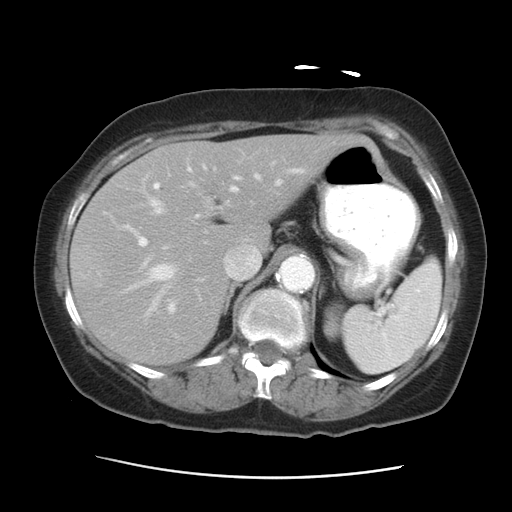
Contrast-enhanced abdominal CT, one axial slice; position 20 of 29 along the scan axis; reconstruction kernel STANDARD; intravenous contrast given; soft-tissue window (W 400 / L 40 HU); 7.5 mm slice thickness; 512 × 512 image matrix. Female patient, age 64 years. Case-level facts recorded for this patient, not image findings: diagnosis: colorectal cancer liver metastases, imaged before liver resection; multiple liver metastases: no; largest metastasis: 2.5 cm; chemotherapy before resection: no.
Annotated regions visible in this slice (manually delineated by an expert):
- hepatic veins: bounding box <125,161,305,315> (left, top, right, bottom; pixels)
- liver: <70,134,364,364>
- planned liver remnant (the part of the liver to remain after resection): <70,134,364,290>
- portal vein (with intrahepatic branches): <123,163,238,313>